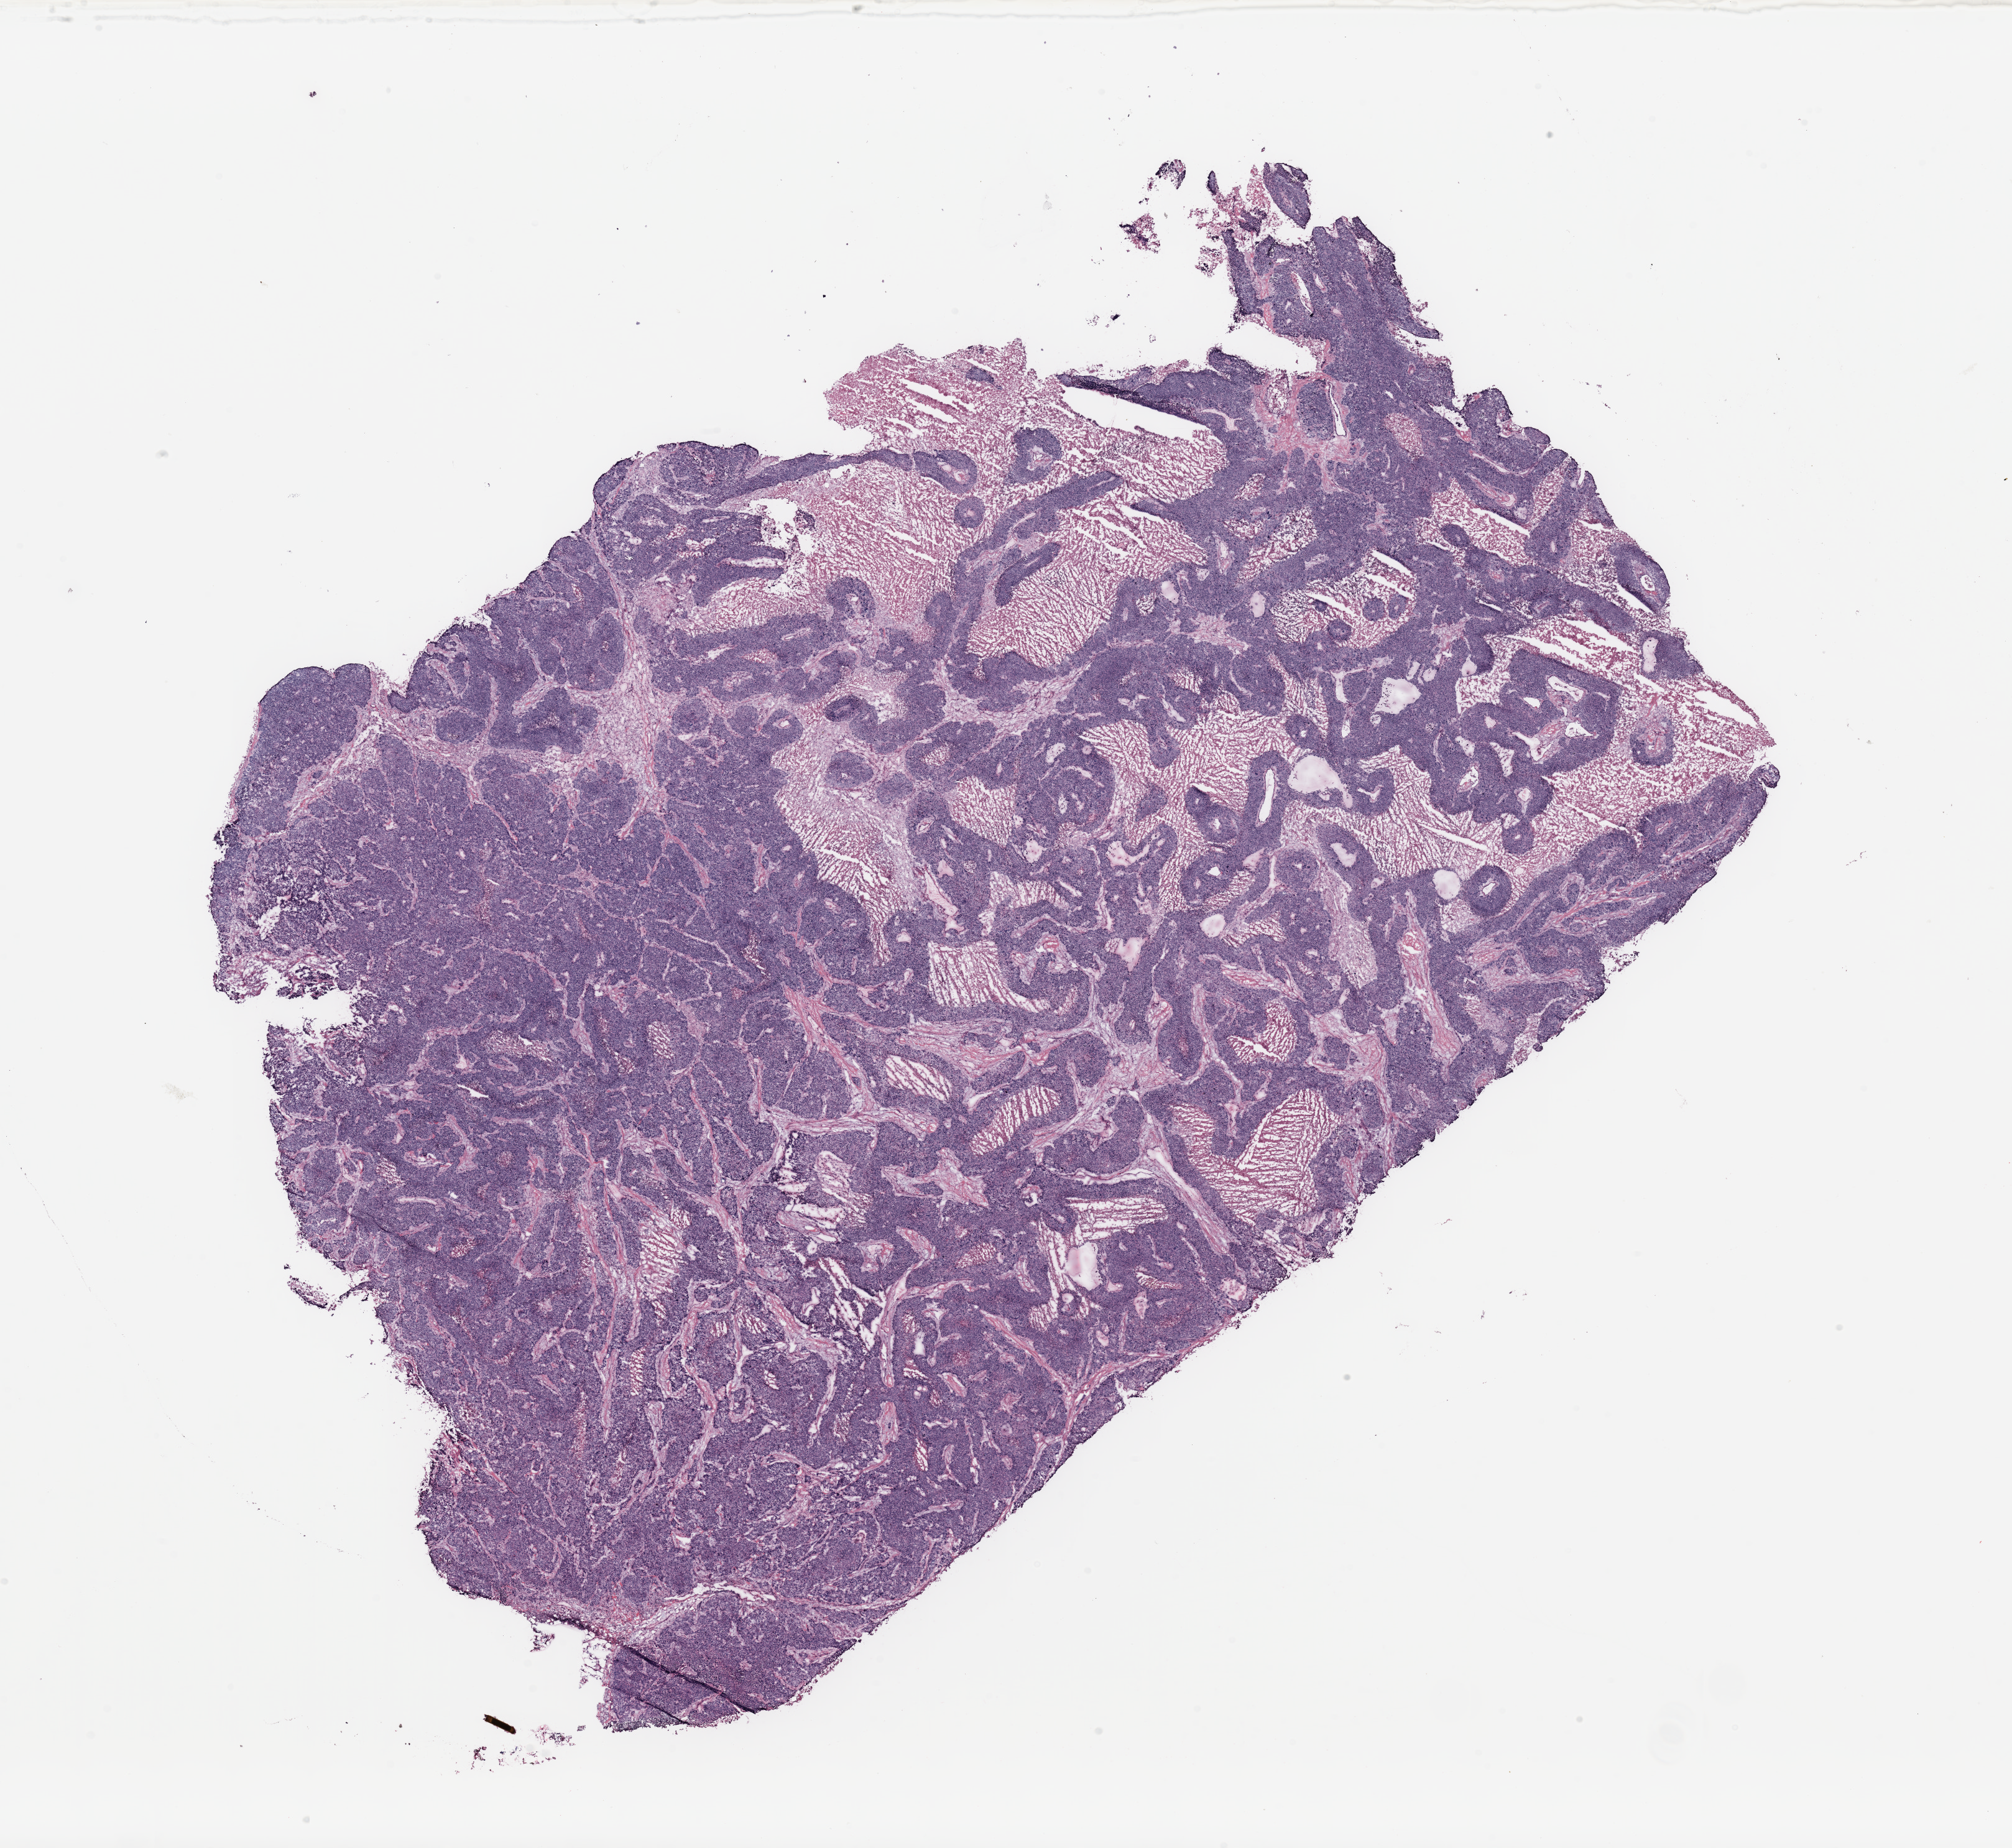
Whole-slide histology image, Hematoxylin and eosin (H&E) stained — a low-resolution overview of the entire scanned area, about 25.6 x 23.5 mm (slide scanned at 20x); breast, tumour tissue. 51-year-old female patient.
Diagnosis: Infiltrating duct carcinoma, NOS.